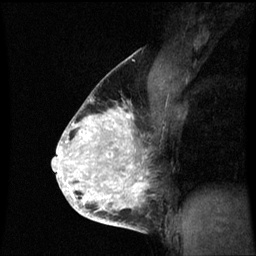
Breast MRI (dynamic contrast-enhanced), one sagittal slice; position 41 of 60 along the scan axis; dynamic contrast-enhanced series, image 2 of 3 at this slice position (ordered by acquisition); 1.5 T; TE 4.2 ms, TR 8.9 ms; 256 × 256 image matrix, field of view 200 × 200 mm. Patient: female, 35 years. Case-level facts recorded for this patient, not image findings: setting: breast cancer imaged before/during neoadjuvant chemotherapy; receptor status: HR-positive, HER2-negative.
Structures marked on this image (semi-automatically segmented with operator editing):
- analysis volume of interest (the breast-tissue region the enhancement analysis was run in; not a lesion): bounding box (x1, y1, x2, y2) in pixels: (66, 100, 159, 215)
- tumour enhancement mask (voxels above the 70 % enhancement threshold inside the analysis volume of interest): (66, 108, 150, 215)